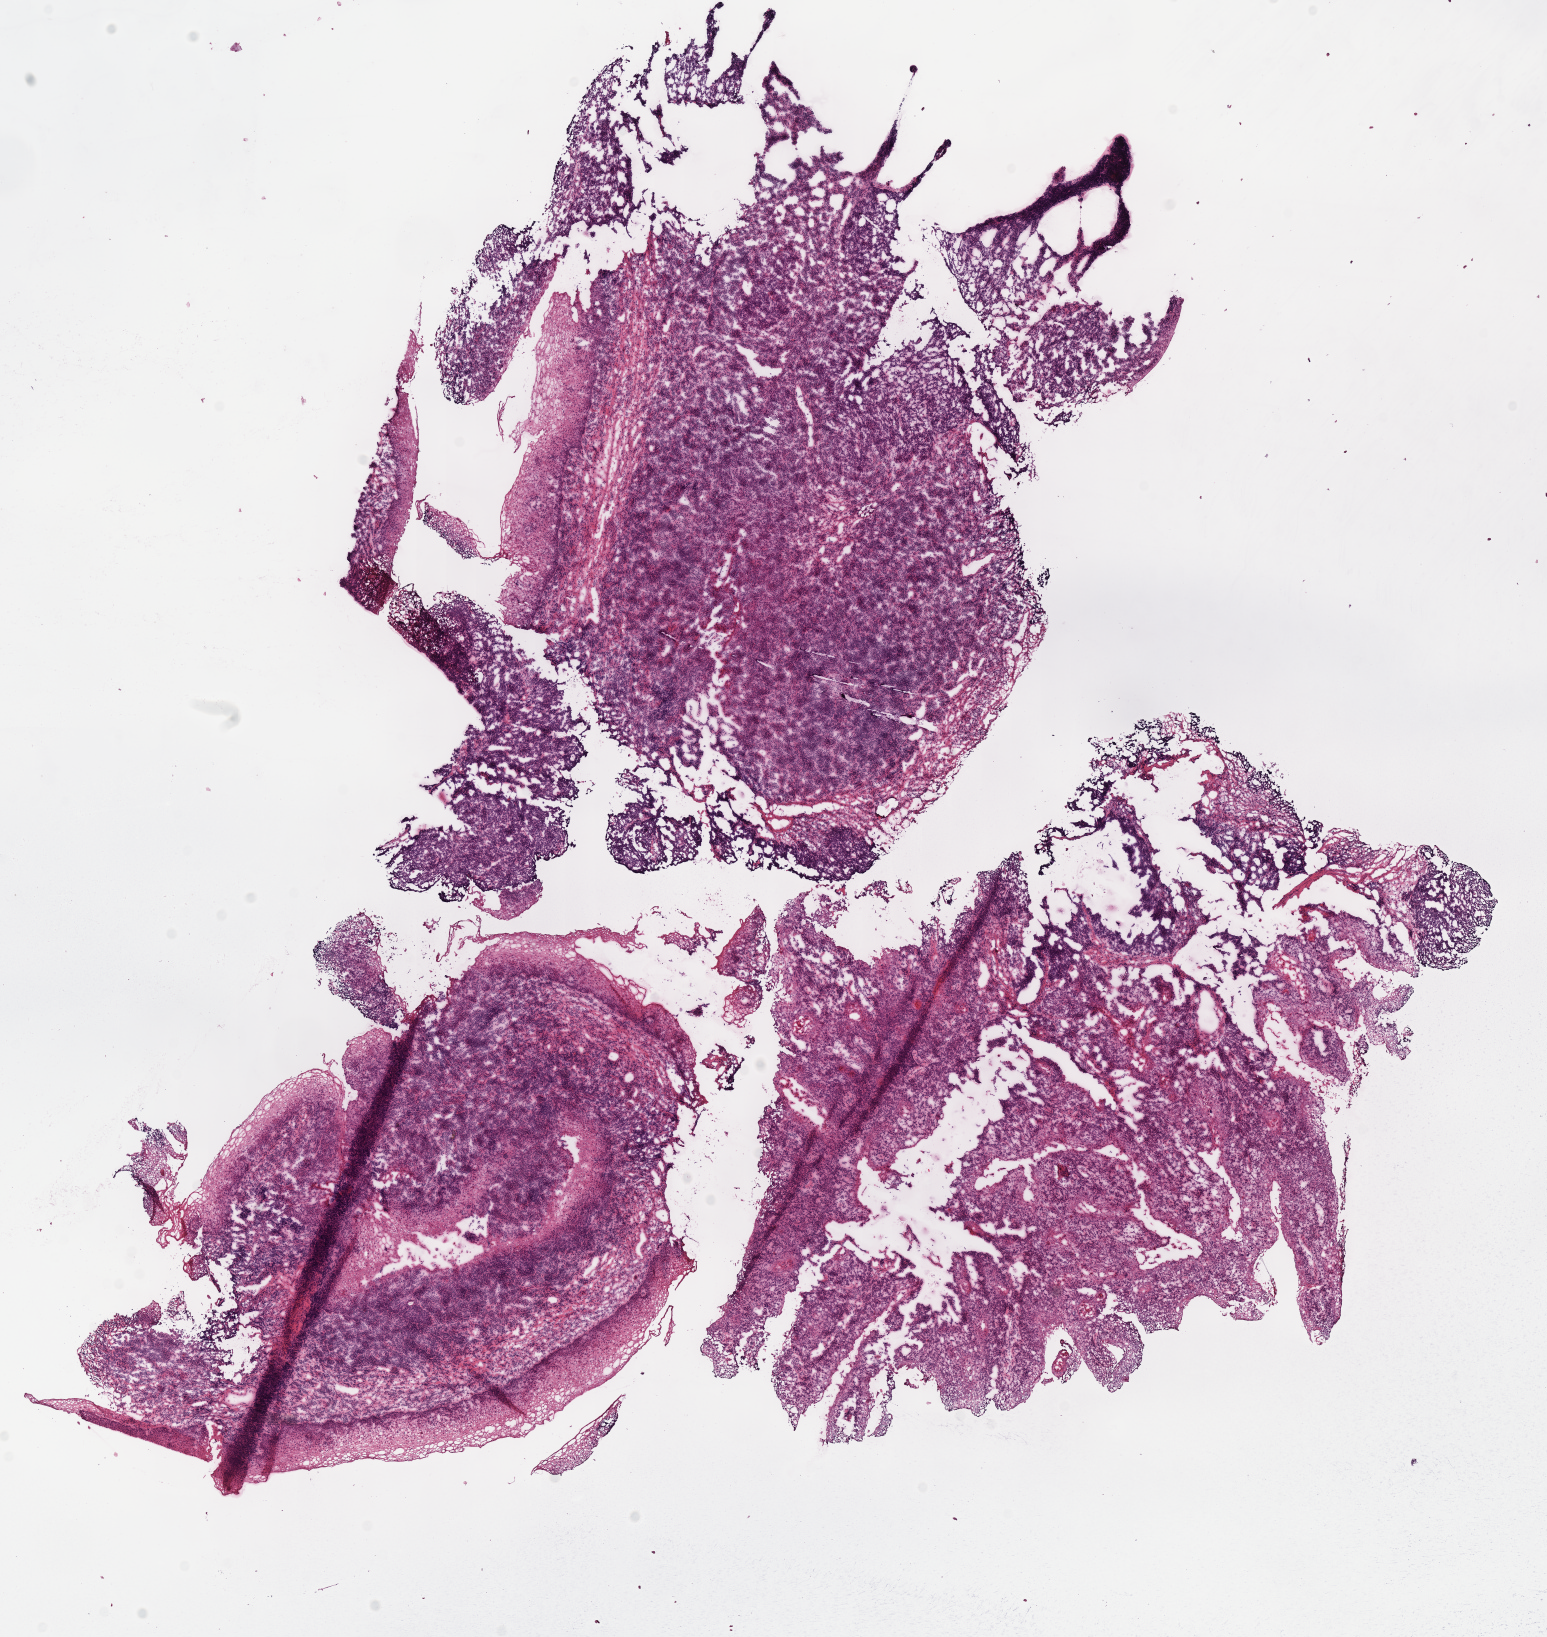
Digitized H&E-stained tissue section (whole slide) — low-resolution overview of the scanned area, about 12.2 x 12.9 mm (slide scanned at 40x), frozen section from the top of the tissue portion, primary tumour sample from the head and neck. Patient: male, age at initial diagnosis 58 years. Histologic grade: G4 (undifferentiated). Pathologist review of this section (percent, as recorded): tumour cells 65%, tumour nuclei 75%, normal cells 25%, stromal cells 10%, necrosis 0%. Inflammatory infiltration, as recorded: lymphocyte infiltration 20%.
* diagnosis: Squamous cell carcinoma, NOS